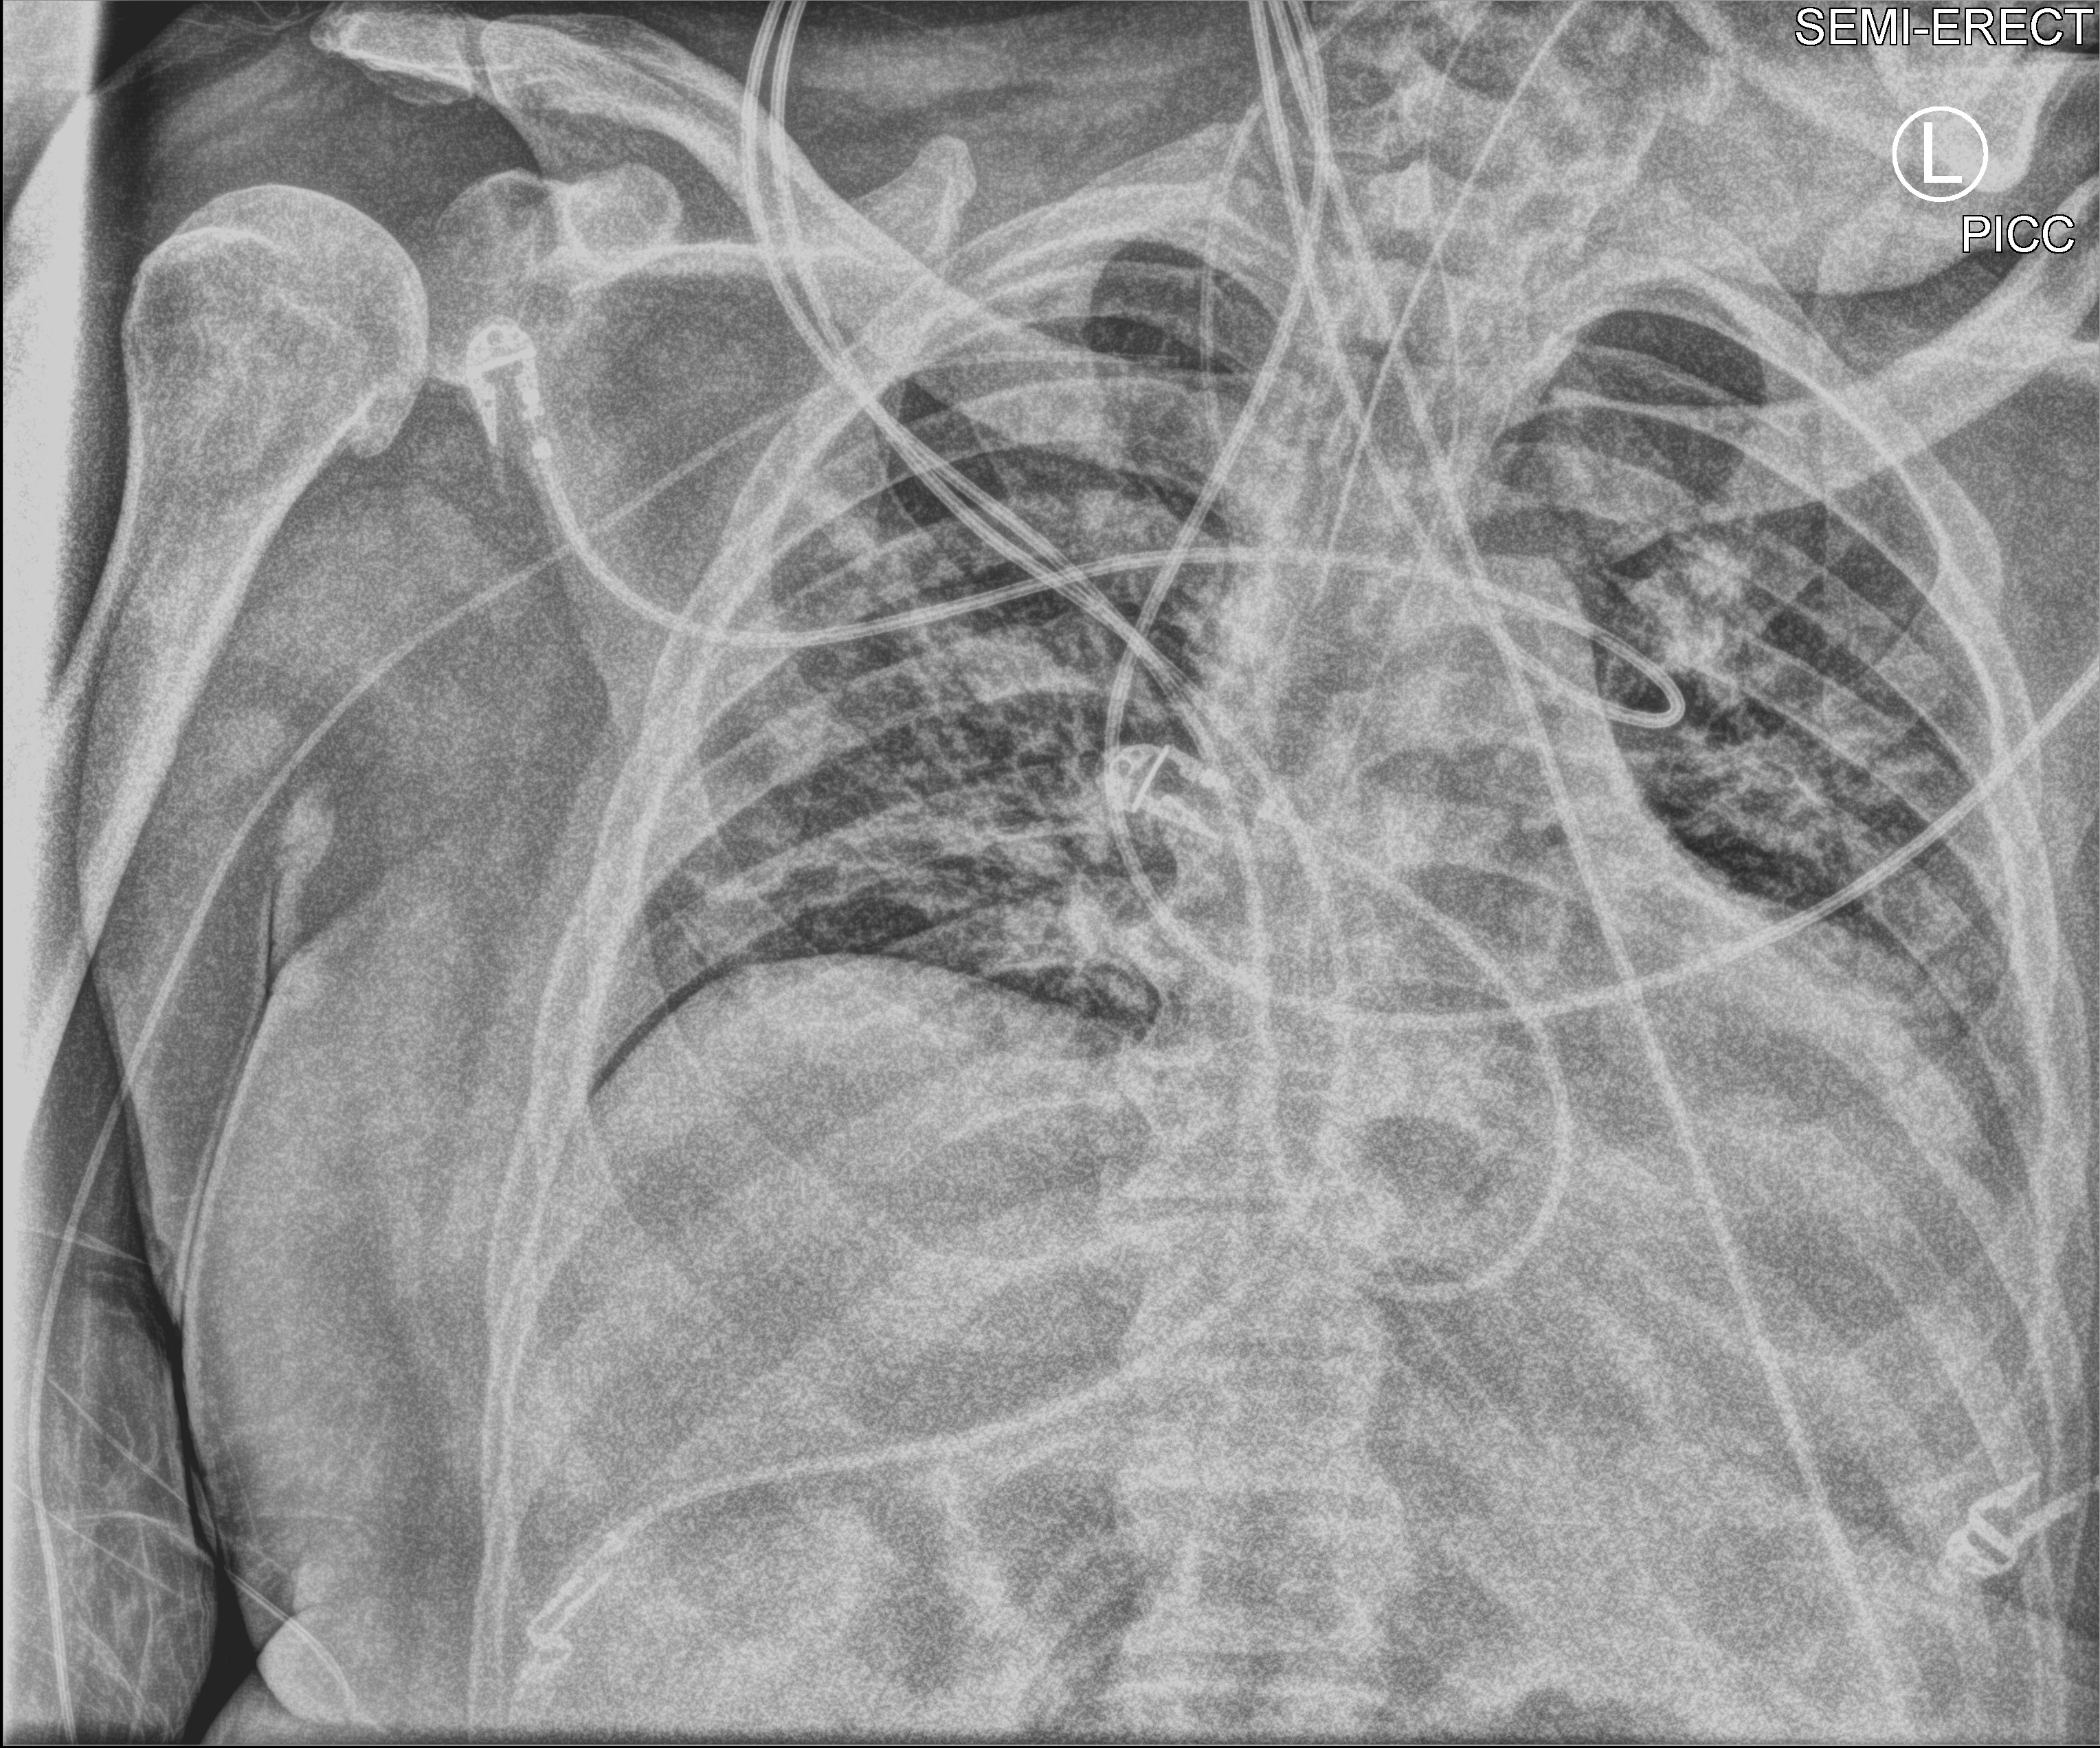
Portable chest radiograph; anteroposterior (AP) projection. Male patient hospitalised with COVID-19, age 18–59 years.
From the hospital-stay record, not from the radiograph (when in the stay this image was taken is not recorded): length of hospital stay: 41 days; smoking status (admission record): never.